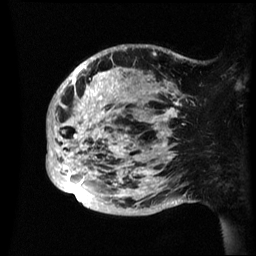
Breast MRI (dynamic contrast-enhanced), one sagittal slice. Position 16 of 60 along the scan axis. Dynamic contrast-enhanced series, image 2 of 3 at this slice position (ordered by acquisition). 1.5 T. TE 4.2 ms, TR 8.4 ms. 2.4 mm slice thickness. 256 × 256 image matrix, field of view 230 × 230 mm. Female patient, age 48 years.
Outlined on this slice (semi-automatic segmentation, software-assisted and operator-edited):
- analysis volume of interest (the breast-tissue region the enhancement analysis was run in; not a lesion): bounding box (x1, y1, x2, y2) in pixels: (47, 45, 195, 216)
- tumour enhancement mask (voxels above the 70 % enhancement threshold inside the analysis volume of interest): (47, 47, 179, 199)